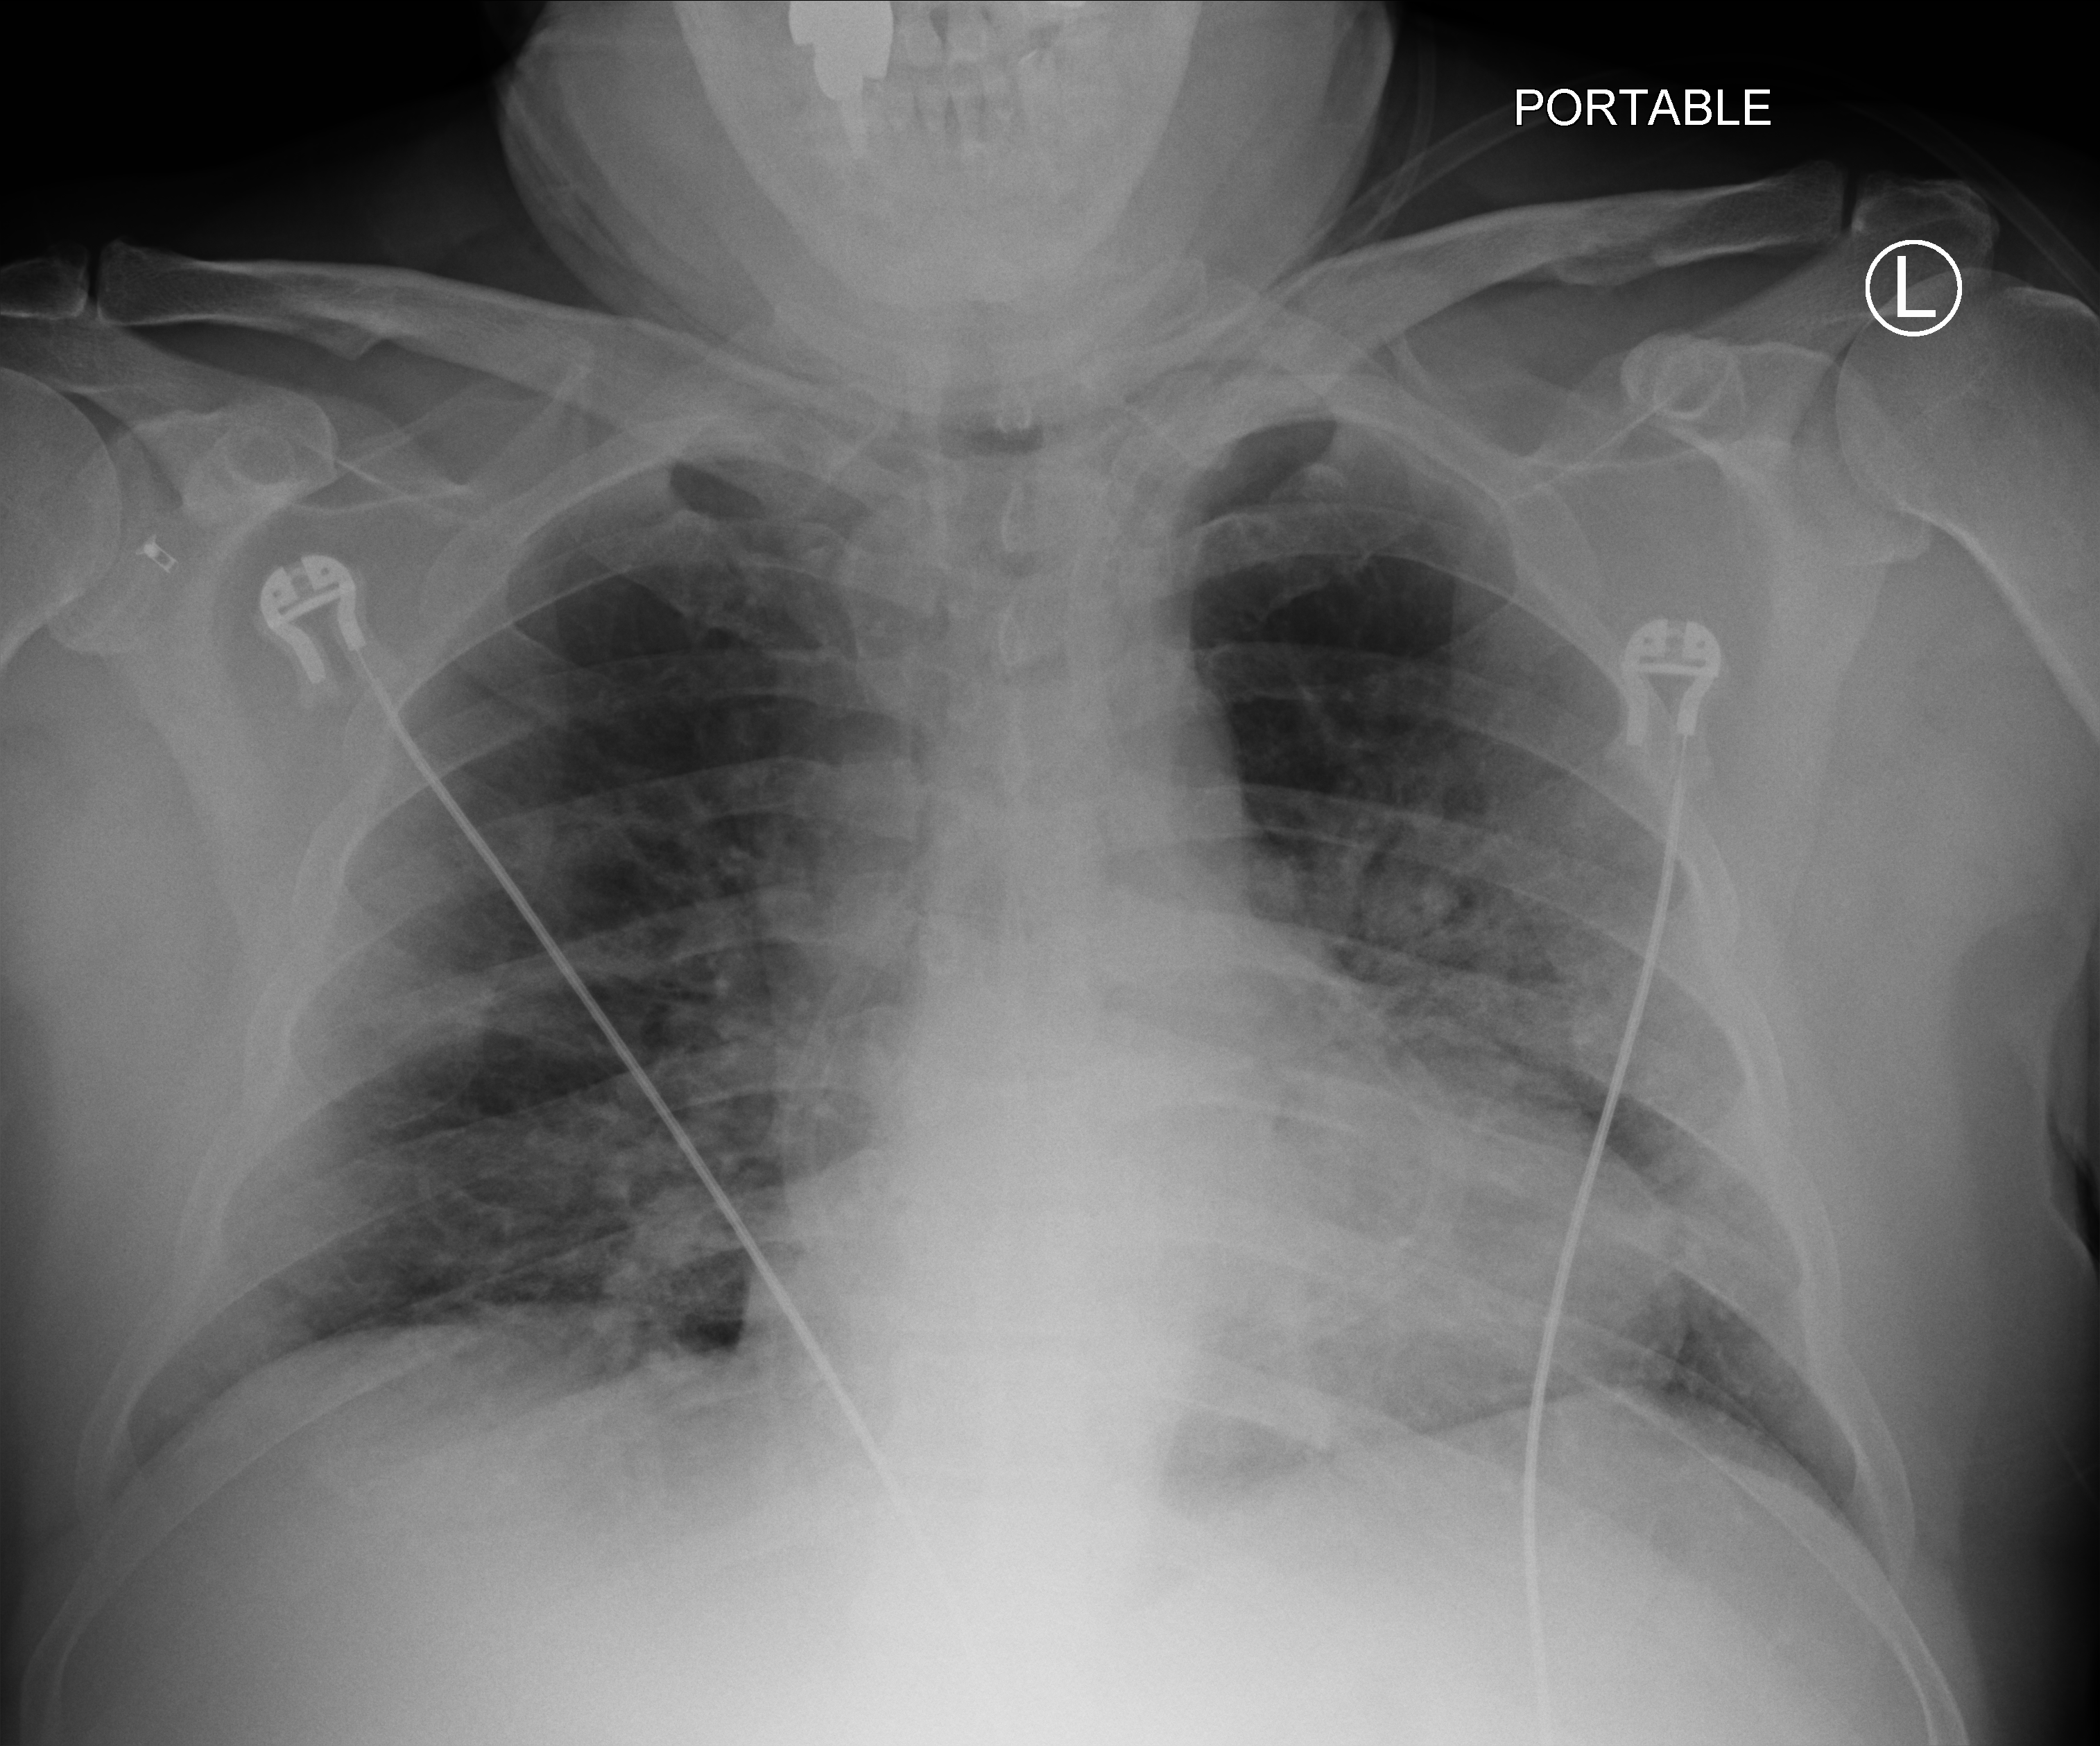
Portable chest radiograph, anteroposterior (AP) projection. Male patient hospitalised with COVID-19, age 18–59 years.
From the hospital-stay record, not from the radiograph (when in the stay this image was taken is not recorded):
- mechanically ventilated during this hospital stay: yes
- length of hospital stay: 52 days